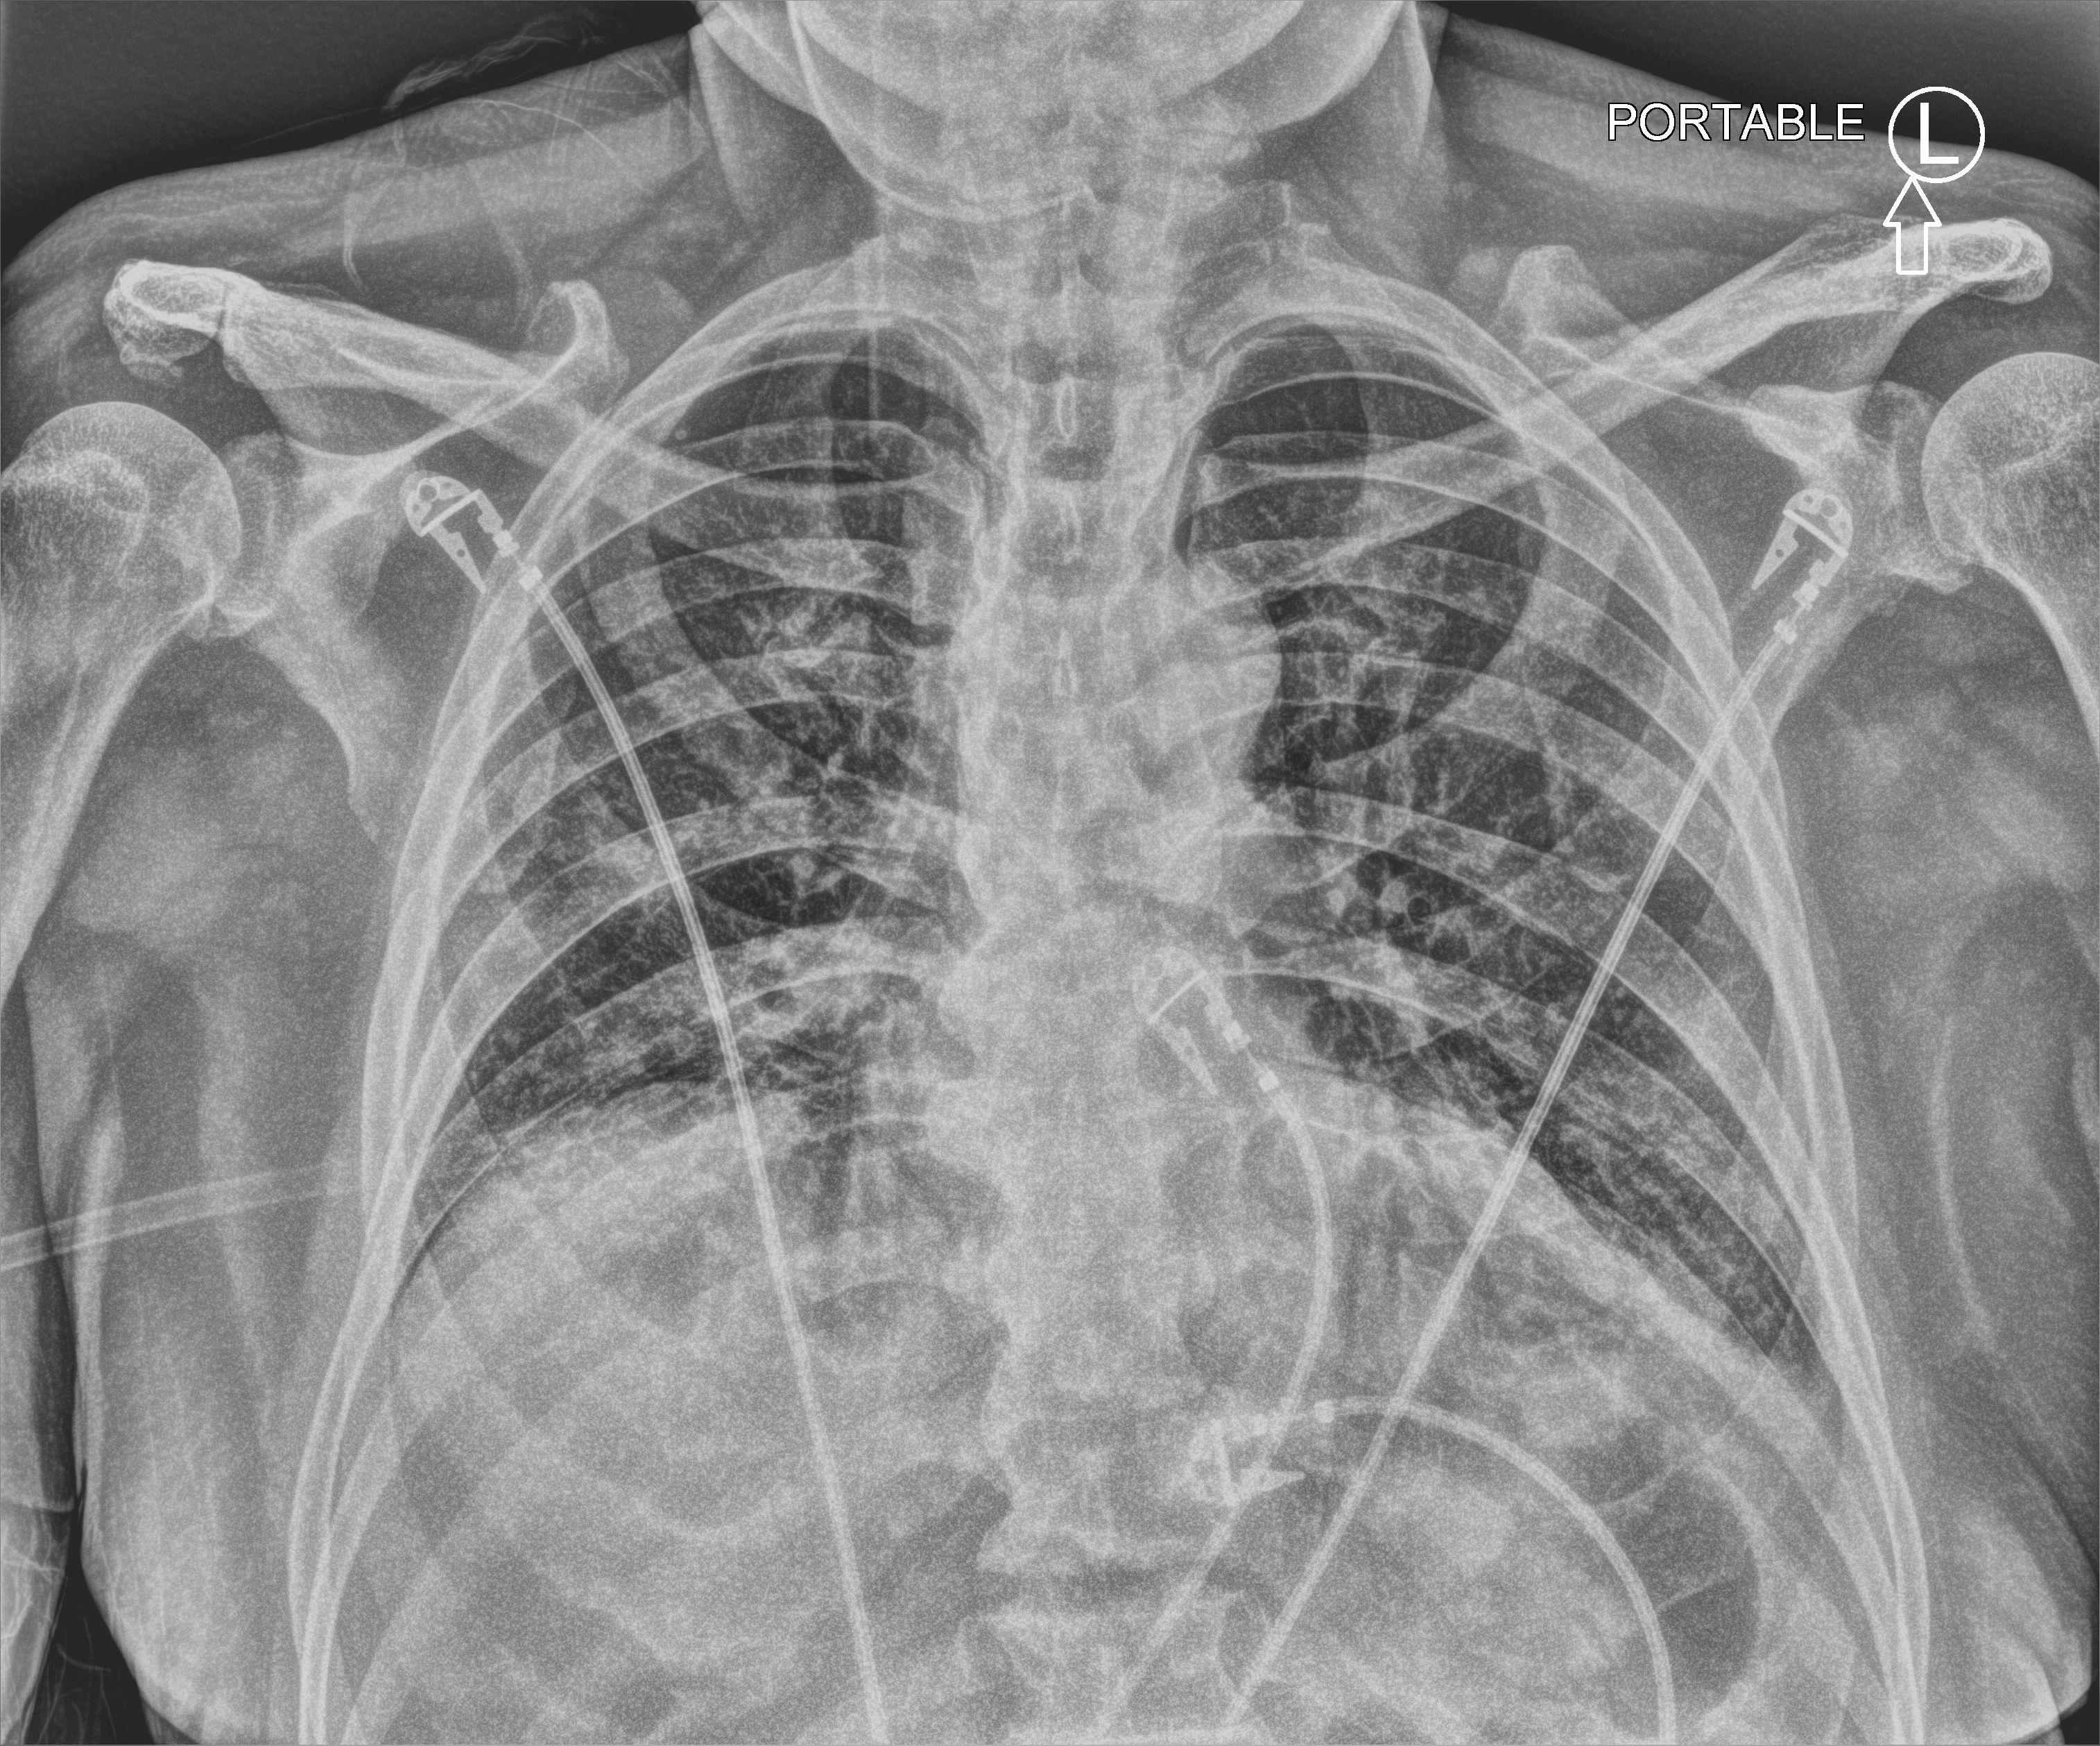
Chest X-ray (portable), anteroposterior (AP) projection. Patient hospitalised with COVID-19; male, aged 75–90 years.
From the hospital-stay record, not from the radiograph (when in the stay this image was taken is not recorded): admitted to intensive care during this hospital stay: yes; chronic kidney disease (admission record): no.